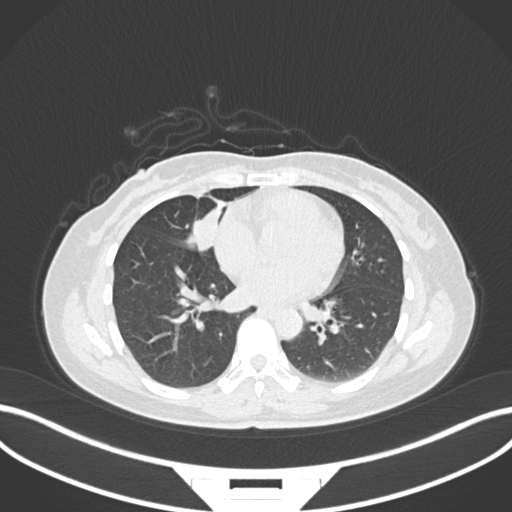
Chest CT, one axial slice. Position 66 of 171 along the scan axis. Reconstruction kernel B30f. 120 kVp. Lung window (W 1500 / L -600 HU). 1 mm slice thickness. 512 × 512 image matrix. Patient: female, 43 years. Case-level facts recorded for this patient, not image findings: clinical TNM (as recorded): T1c N3 M1; histopathological grade: G1.
Annotated regions visible in this slice (rectangle marked by the reading radiologist):
- lung tumour (recorded histology: adenocarcinoma): bounding box <186,207,220,258> (left, top, right, bottom; pixels)